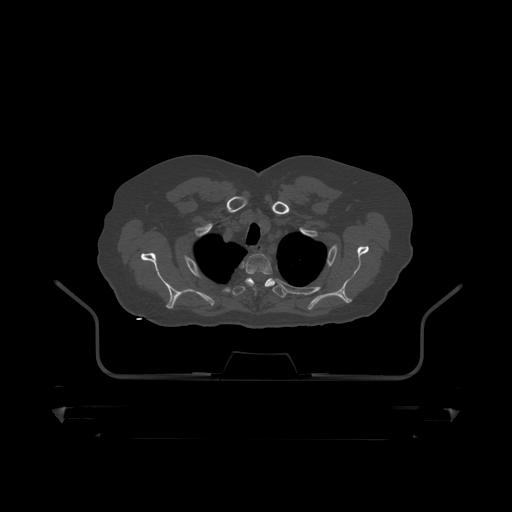
CT including the spine, one axial slice. Slice 369 of 390 in the series (ordered by position). 120 kVp. Bone window (W 1800 / L 400 HU). 1.25 mm slice thickness. 512 × 512 image matrix, field of view 650 × 650 mm. Male patient, age 60 years. From the clinical record (not read from this slice): primary cancer: prostate.
Structures marked on this image (semi-automatic segmentation, software-assisted and operator-edited):
- T2 vertebra: box from (x=246, y=254) to (x=273, y=286) px
- T3 vertebra: (x=233, y=278)–(x=287, y=298)